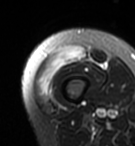
MRI of an extremity soft-tissue mass, one axial slice. Slice 9 of 95 in the series (ordered by position). T2-weighted fat-saturated. MR volume resampled by the dataset authors to the PET/CT grid (not the native acquisition matrix). 135 × 146 image matrix, field of view 132 × 143 mm. Female patient. From the clinical record (not read from this slice): histological type: pleiomorphic undifferentiated sarcoma; grade: high; site of the primary tumour: right quadricep.
Structures marked on this image (expert contour drawn on MRI and transferred to this co-registered scan by the dataset authors):
- gross tumour volume including surrounding oedema: box from (x=37, y=45) to (x=86, y=96) px